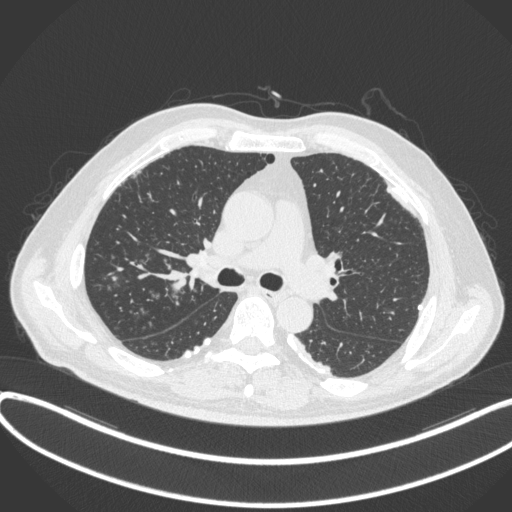
Chest CT, one axial slice. Position 261 of 455 along the scan axis. Reconstruction kernel B31f. 120 kVp. Lung window (W 1500 / L -600 HU). 512 × 512 image matrix, field of view 400 × 400 mm. Patient: male, 58 years. From the clinical record (not read from this slice): clinical TNM (as recorded): T1c N0 M0.
Structures marked on this image (bounding box drawn by a radiologist):
- lung tumour (recorded histology: squamous cell carcinoma): bounding box (x1, y1, x2, y2) in pixels: (162, 267, 192, 296)